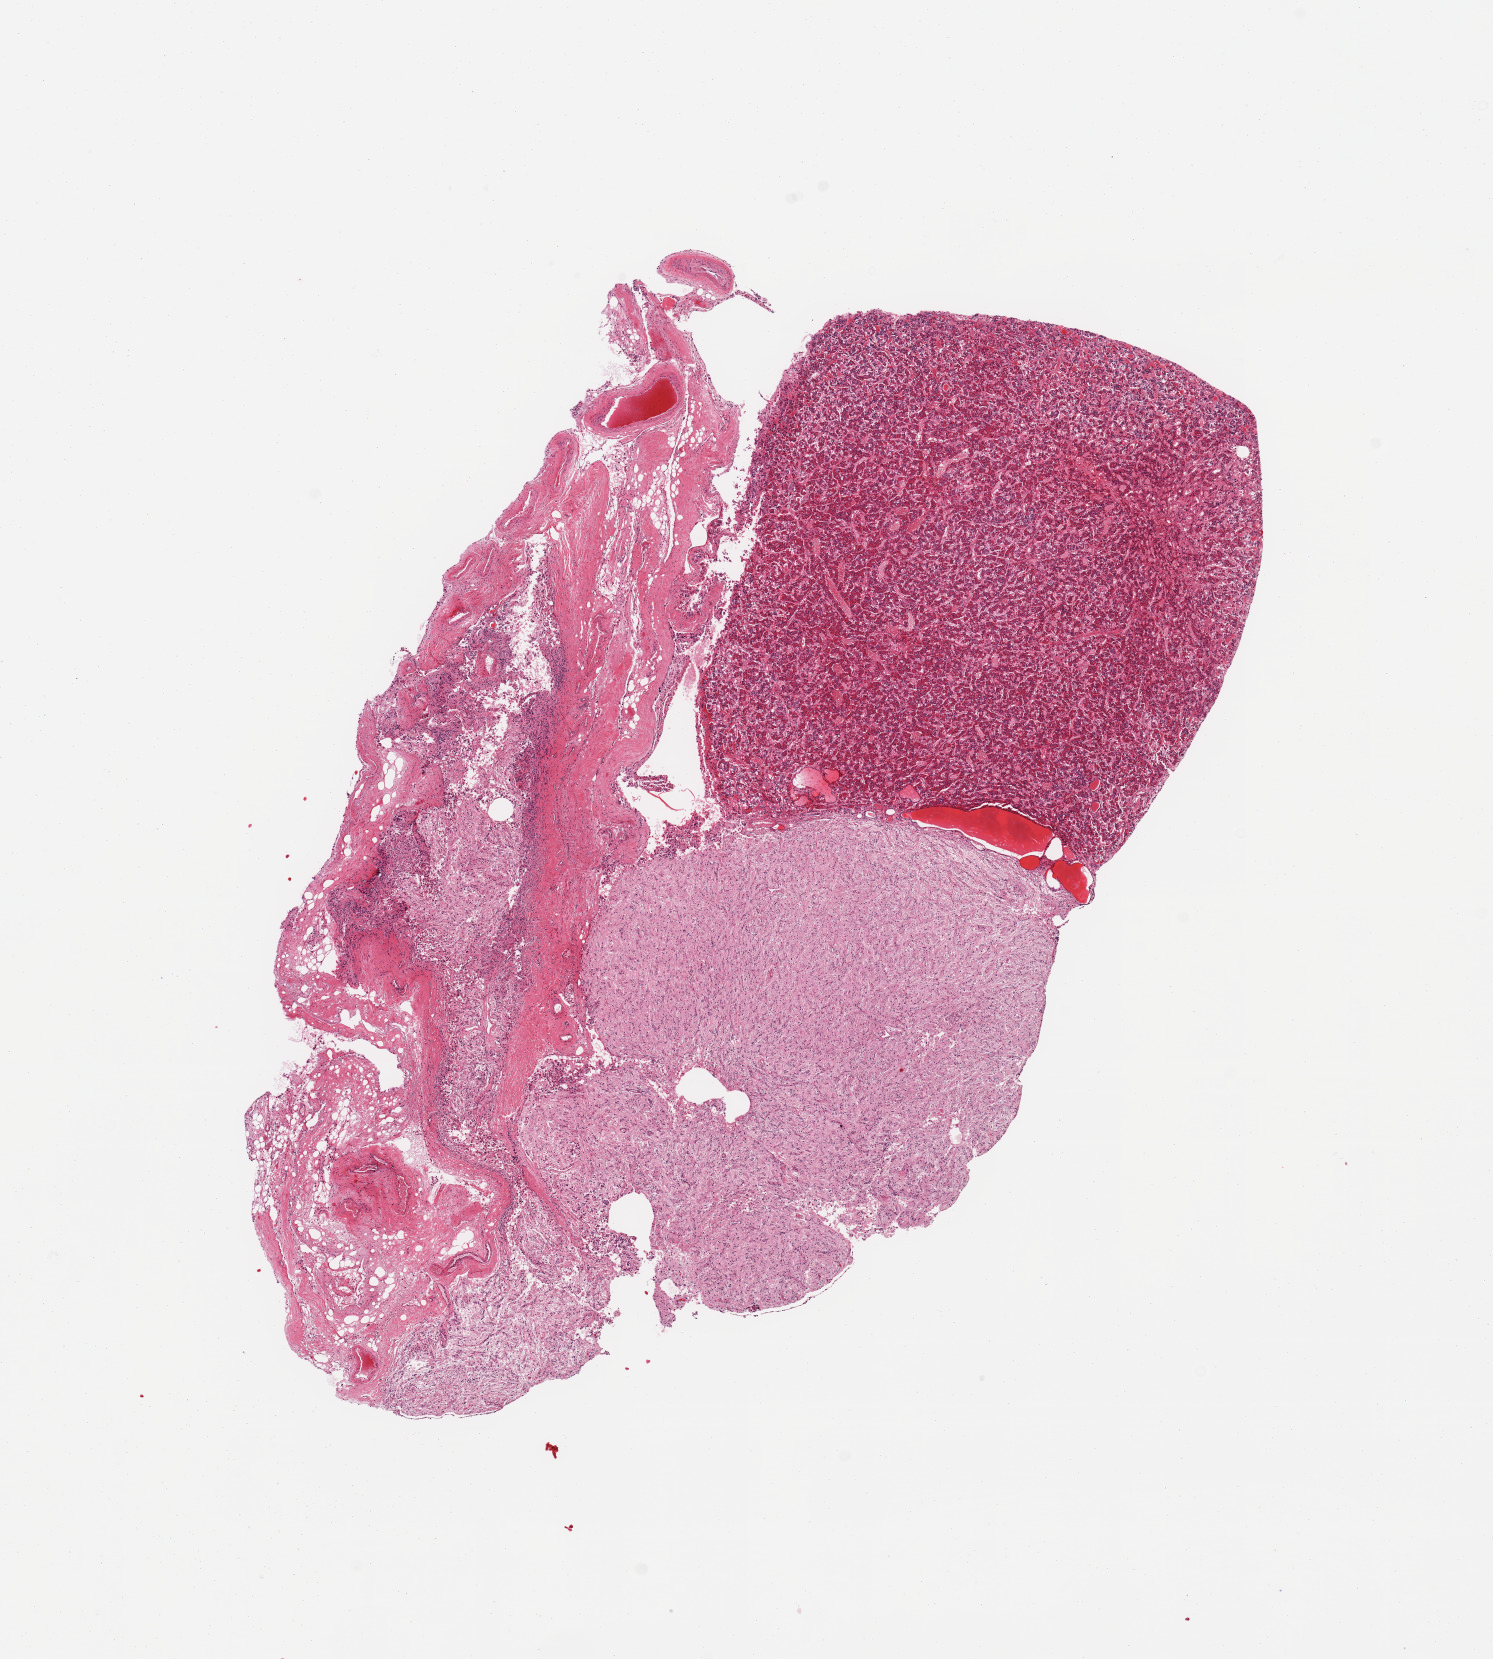
Hematoxylin and eosin (H&E) whole-slide image — whole scanned area (about 11.8 x 13.1 mm) shown as a low-resolution overview. PAXgene-fixed, paraffin-embedded tissue. Target tissue: pituitary. Donor tissue sample. Donor: male.
Pathologist's review note for this sample: 1 piece; equal amounts of anterior & posterior lobes.